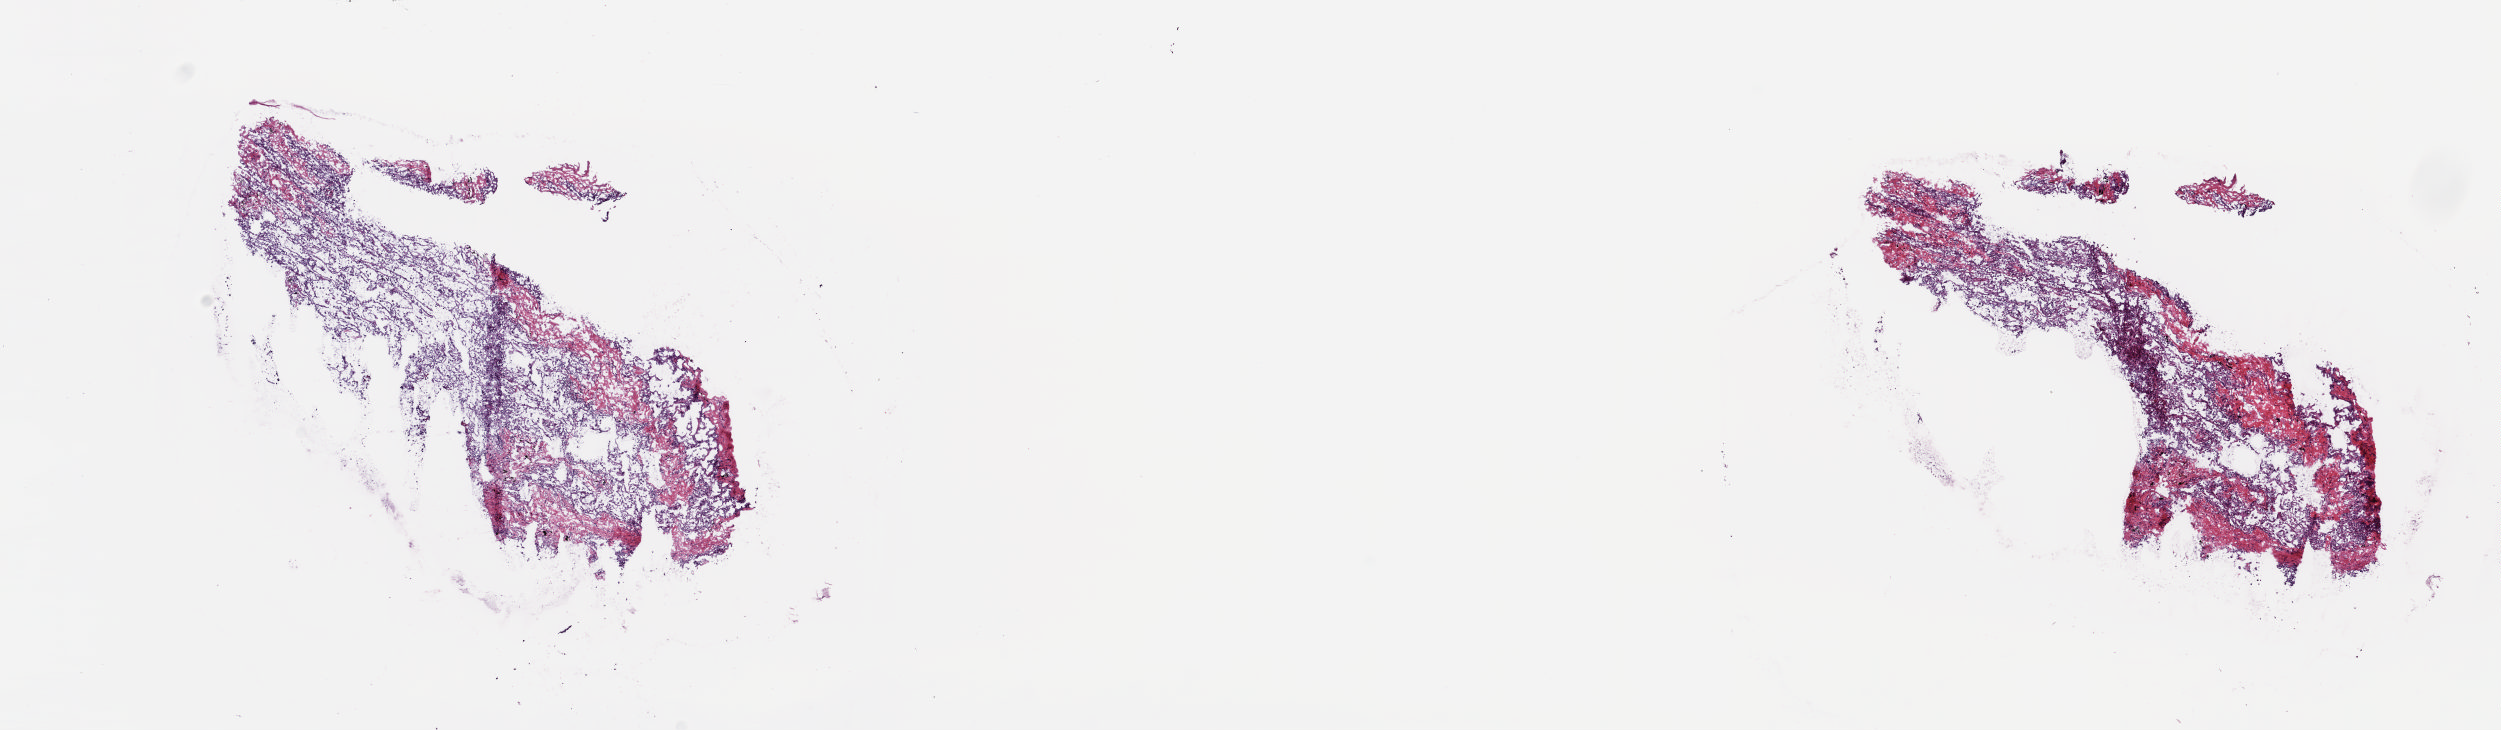
Digitized H&E tissue section (whole slide), a low-resolution overview of the entire scanned area, about 19.8 x 5.8 mm; frozen section from the top of the tissue portion; solid tissue normal (non-tumour tissue) sample from the lung. Male, age 69 years at initial diagnosis. Pathologist review of this section (percent, as recorded): tumour cells 0%, tumour nuclei 0%, normal cells 60%, stromal cells 38%, necrosis 2%. Inflammatory infiltration, as recorded: lymphocyte infiltration 3%, monocyte infiltration 8%, neutrophil infiltration 2%.
• this section: solid tissue normal sample (biorepository sample class)
• patient diagnosis: Adenocarcinoma, NOS (upper lobe, lung)